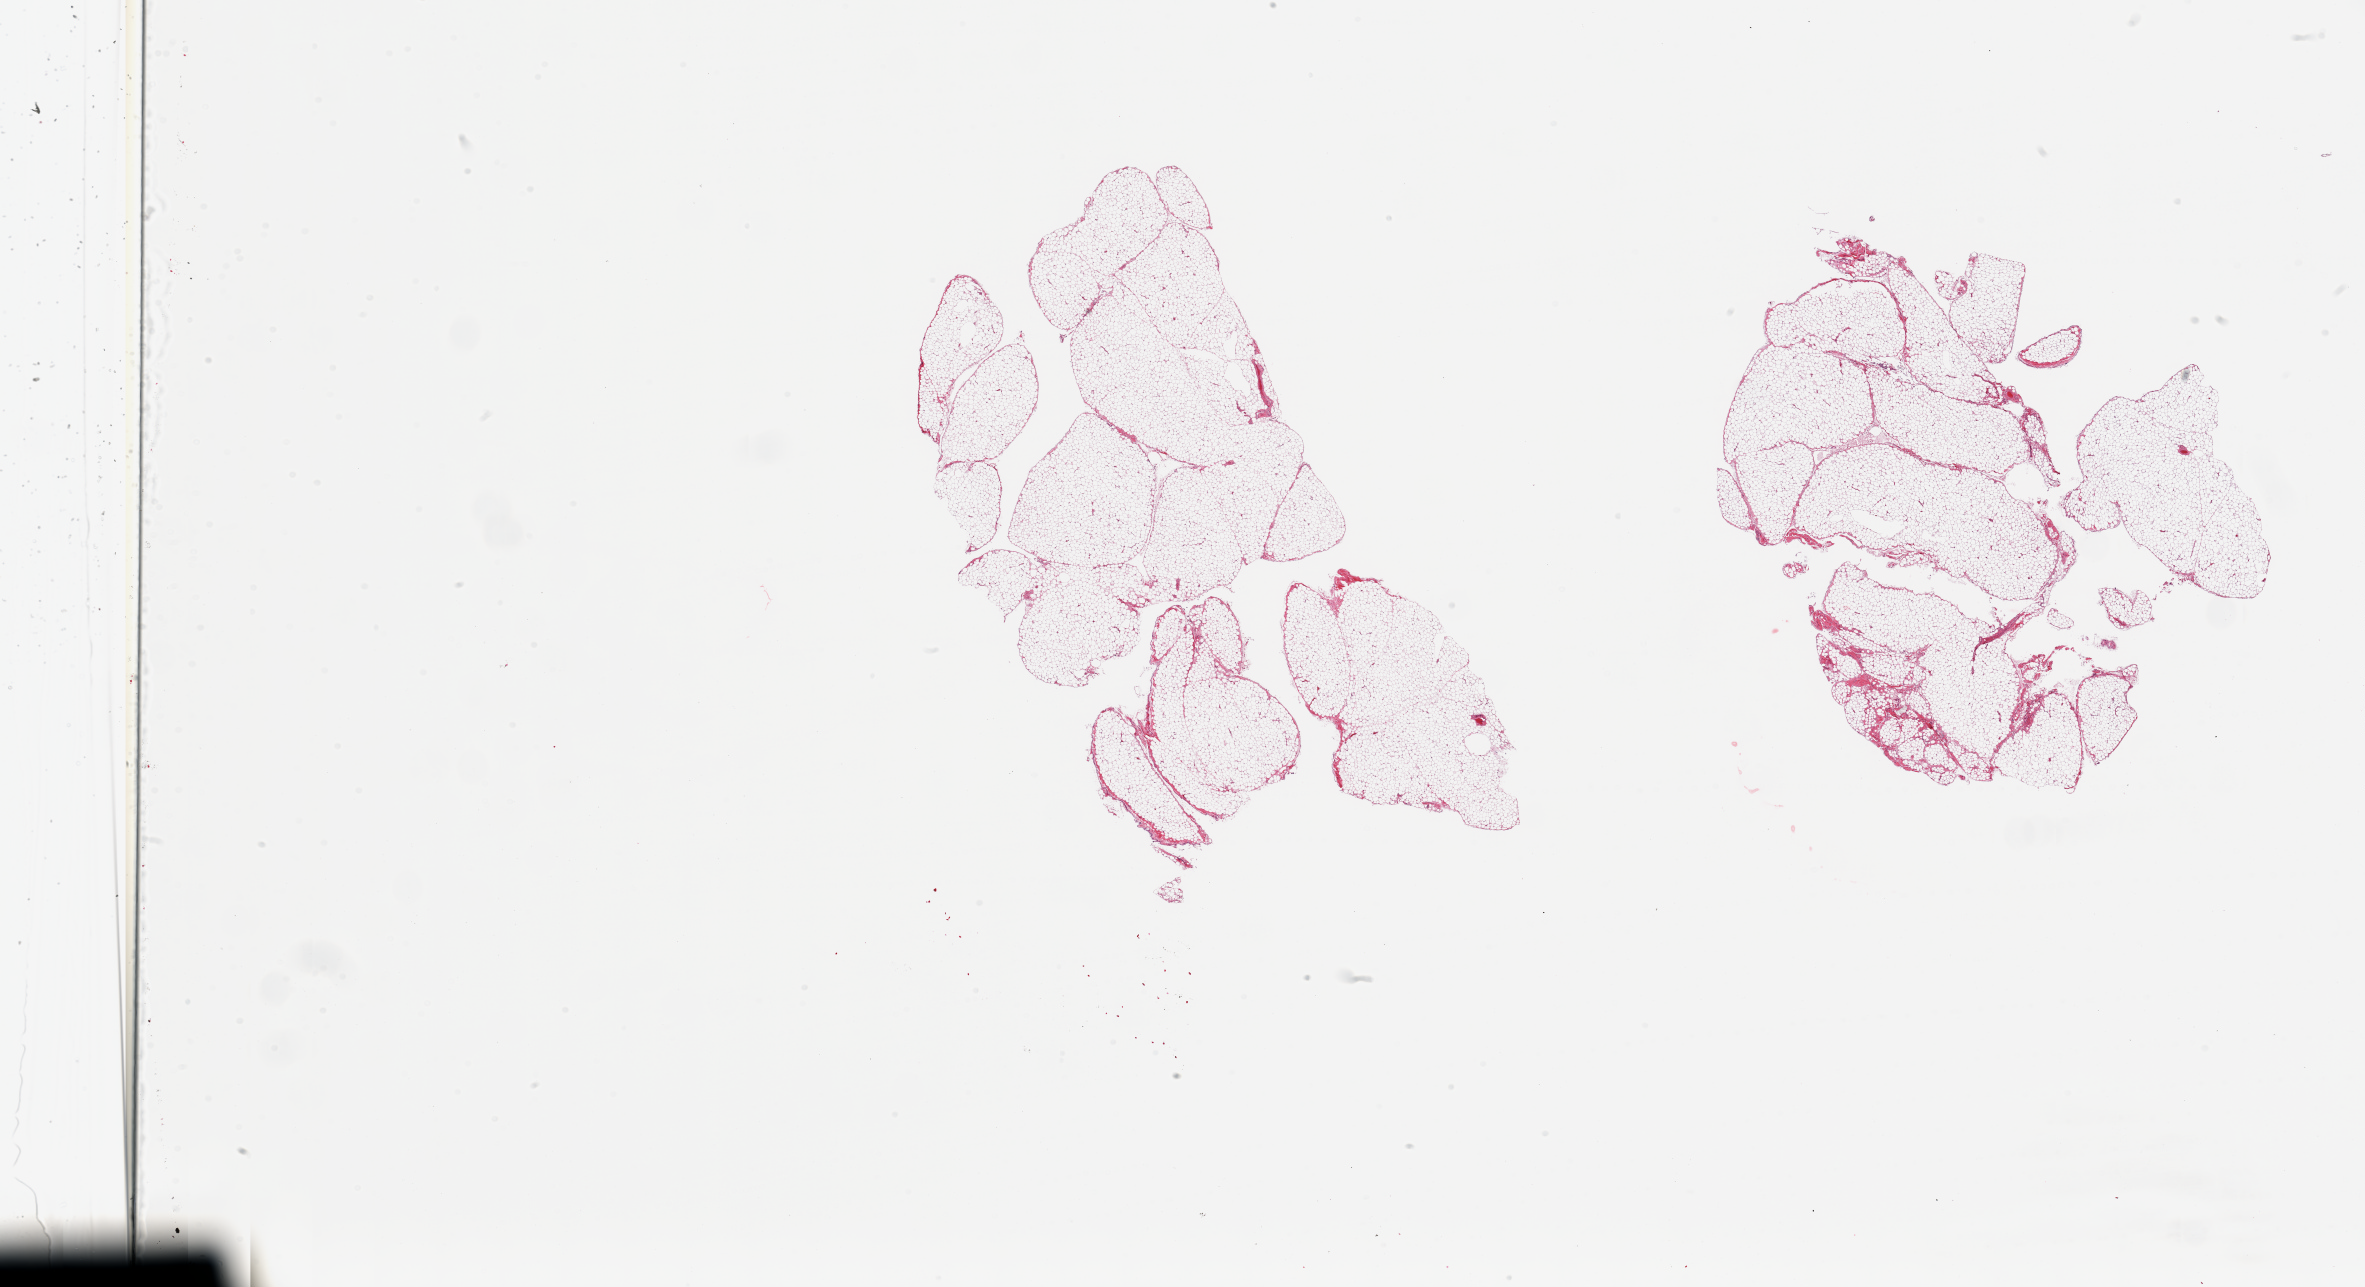
Haematoxylin and eosin whole-slide image, brightfield — shown as a low-resolution overview of the whole scanned area (about 37.4 x 20.4 mm); PAXgene-fixed, paraffin-embedded tissue; section of omentum (target tissue); tissue donor sample.
Reviewer comment on this tissue sample: 2 pieces; <5% stromal content.